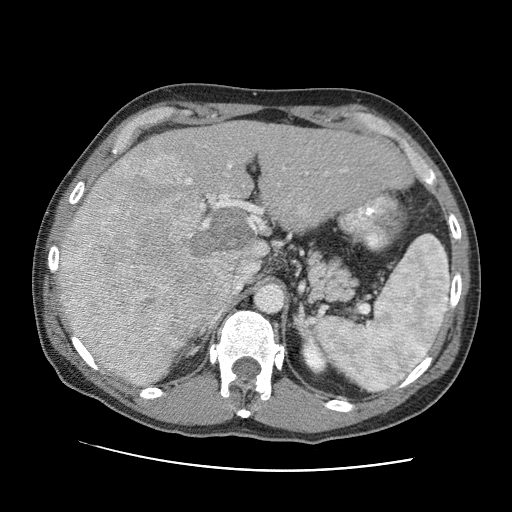
Contrast-enhanced abdominal CT (liver protocol), one axial slice. Slice 54 of 95 in the series (ordered by position). Reconstruction kernel STANDARD. One of 2 acquisitions stored at this slice position. Soft-tissue window (W 400 / L 40 HU). 2.5 mm slice thickness. 512 × 512 image matrix, field of view 360 × 360 mm. From the clinical record (not read from this slice): diagnosis: hepatocellular carcinoma (patient treated with transarterial chemoembolisation; whether this scan precedes or follows treatment is not stated here); TNM stage (as recorded): Stage-IVA; Child-Pugh class: A.
Annotated regions visible in this slice (semi-automatic segmentation, software-assisted and operator-edited):
- abdominal aorta: bounding box (x1, y1, x2, y2) in pixels: (256, 284, 282, 311)
- liver parenchyma outside the tumour (the mass and vessels are separate outlines, so this box may not span the whole liver): (60, 120, 412, 386)
- mass: (60, 150, 267, 383)
- liver vessels: (135, 146, 346, 384)